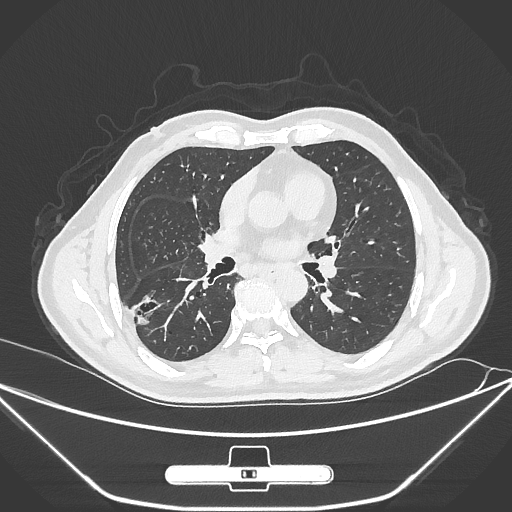
Chest CT, one axial slice; slice 151 of 310 in the series (ordered by position); 120 kVp; lung window (W 1500 / L -600 HU); 1 mm slice thickness; 512 × 512 image matrix, field of view 398 × 398 mm. Male patient, age 71 years. Case-level facts recorded for this patient, not image findings: clinical TNM (as recorded): T1c N0 M0.
Outlined on this slice (bounding box drawn by a radiologist):
- lung tumour (recorded histology: adenocarcinoma): bounding box <127,292,166,330> (left, top, right, bottom; pixels)